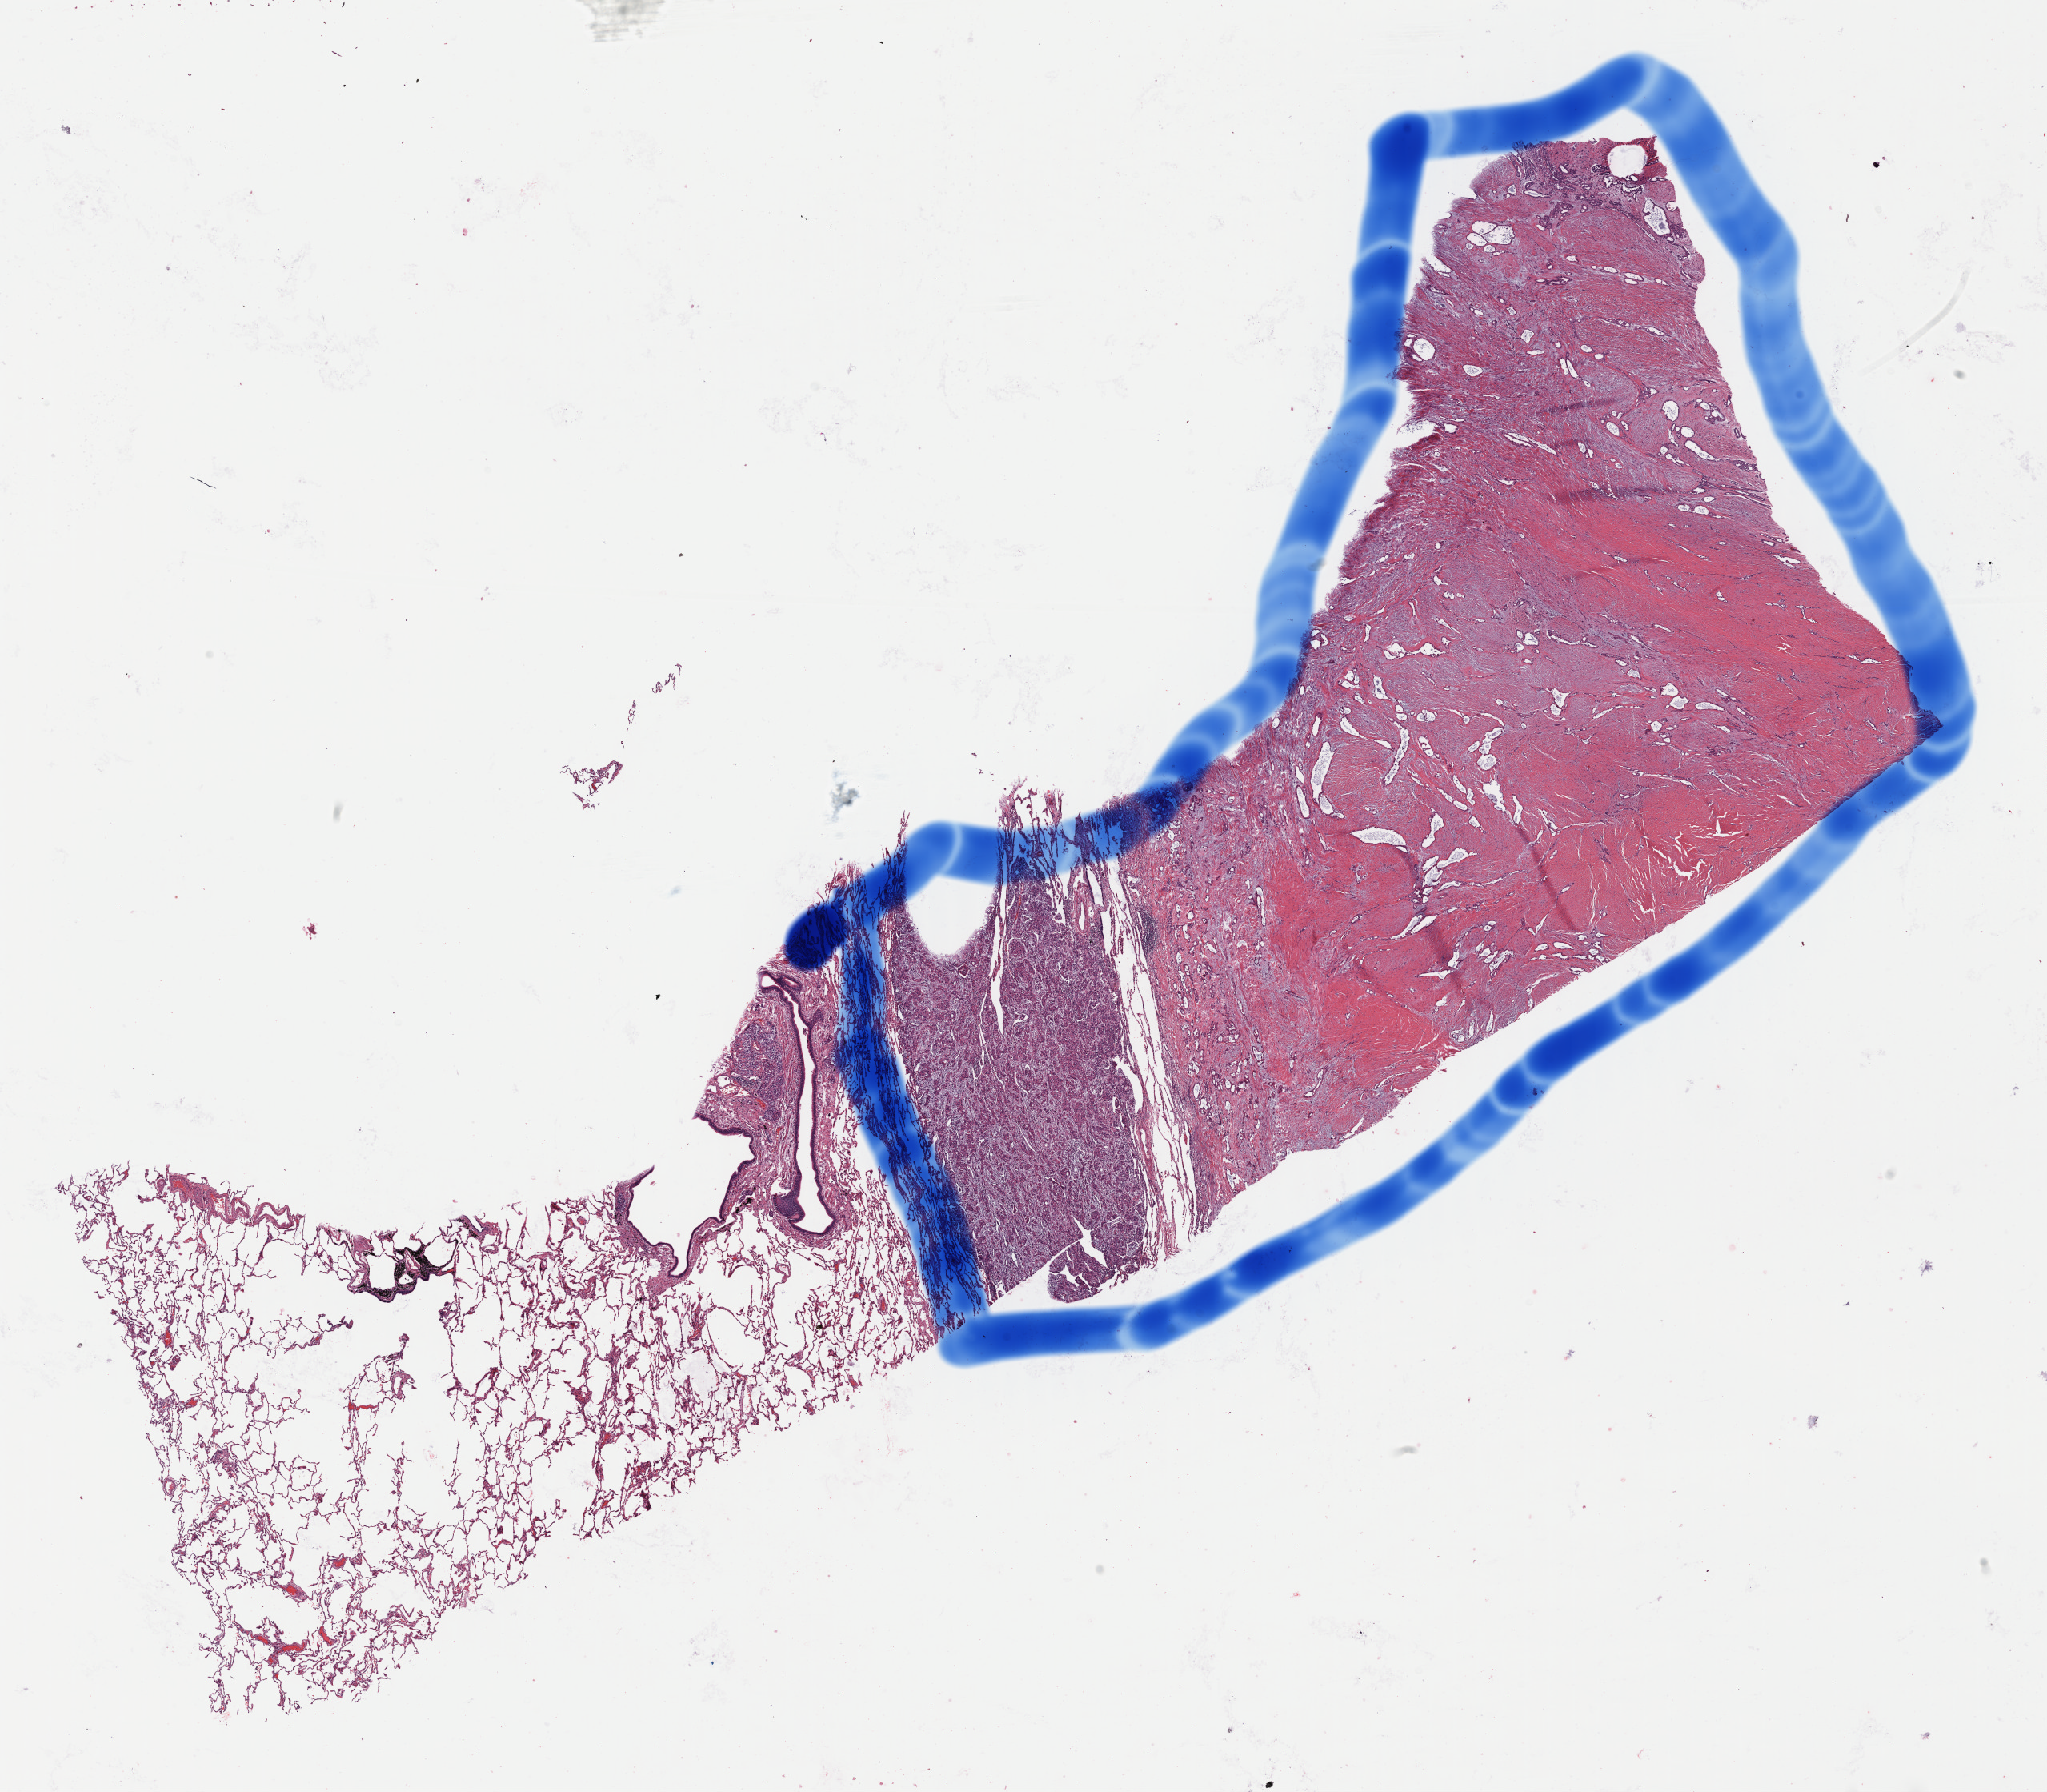
Digitized Hematoxylin and eosin (H&E) stained tissue section (whole slide) — whole scanned area (about 20.2 x 17.7 mm) shown as a low-resolution overview; formalin-fixed paraffin-embedded (FFPE) diagnostic section; mesothelium, primary tumour sample. Male, age 58 years at initial diagnosis.
AJCC pathologic stage: II. Histologic diagnosis: Epithelioid mesothelioma, malignant (pleura, NOS).